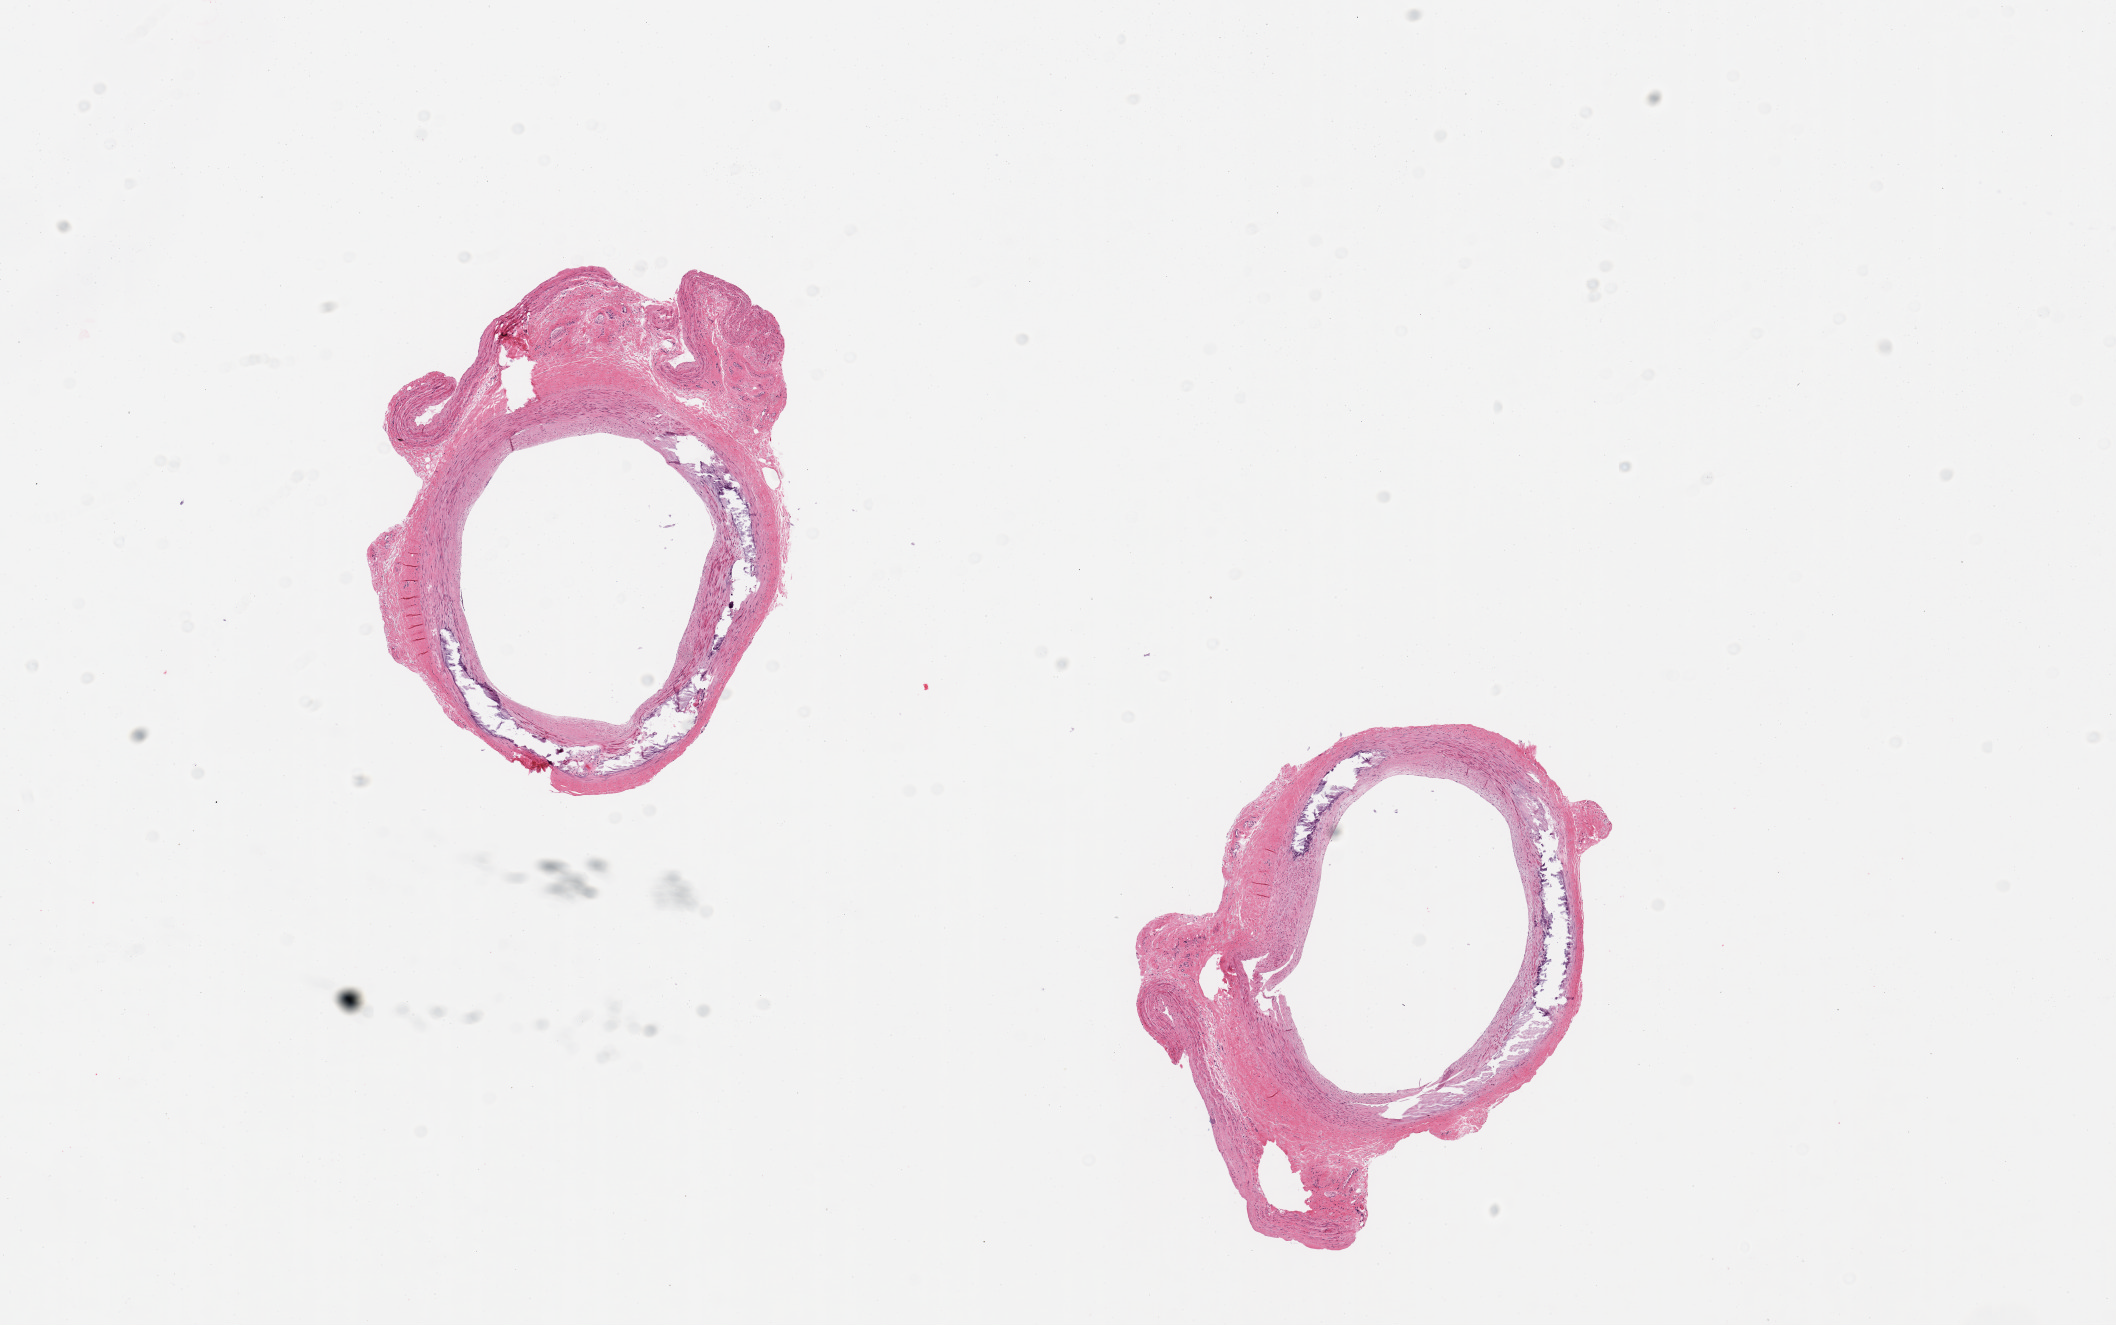
Digitized H&E-stained section — shown as a low-resolution overview of the whole scanned area (about 16.7 x 10.5 mm, from a 20x scan), PAXgene-fixed, paraffin-embedded tissue, sampled site (target tissue): tibial artery, tissue donor sample.
Reviewer comment on this tissue sample: 2 pieces; medial calcificationand atherosclerotic plaque with luminal narrowing by 25%.